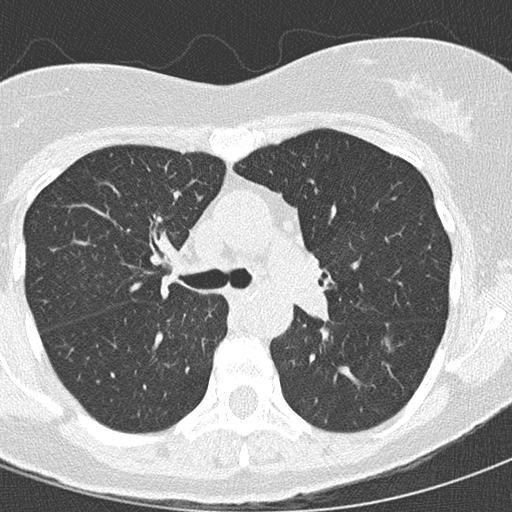
Axial slice from a low-dose chest CT screening exam, baseline screening round, lung window (W 1500 / L -600 HU), 2 mm slice thickness, 512 × 512 image matrix, field of view 270 × 270 mm. Female, age 68 years at enrolment. Current smoker at enrolment.
Expert reader's lesion annotation, bounding box (x1, y1, x2, y2) in pixels: (372, 325, 418, 365). Screening reader's record for this exam (one nodule recorded; not confirmed to be the boxed lesion): non-calcified nodule or mass ≥4 mm, left lower lobe, 15 × 15 mm, mixed attenuation. Official screen result: positive, change unspecified: nodule(s) >= 4 mm or enlarging nodule(s), mass(es), or other non-specific abnormalities suspicious for lung cancer. Participant outcome: lung cancer diagnosed 72 days after this screen — bronchiolo-alveolar adenocarcinoma, NOS, left lower lobe, stage IIIB (AJCC 6th edition), 12 mm at pathology.